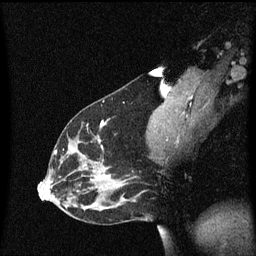
Breast MRI (dynamic contrast-enhanced), one sagittal slice; position 32 of 60 along the scan axis; dynamic contrast-enhanced series, image 2 of 3 at this slice position (ordered by acquisition); 1.5 T; TE 4.2 ms, TR 8.4 ms; 2 mm slice thickness; 256 × 256 image matrix, field of view 200 × 200 mm. Female patient, age 33 years.
Structures marked on this image (semi-automatically segmented with operator editing):
- analysis volume of interest (the breast-tissue region the enhancement analysis was run in; not a lesion): box from (x=45, y=114) to (x=152, y=191) px
- tumour enhancement mask (voxels above the 70 % enhancement threshold inside the analysis volume of interest): (x=55, y=120)–(x=112, y=181)